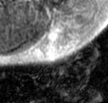
MRI of an extremity soft-tissue mass, one axial slice. Slice 33 of 42 in the series (ordered by position). T2-weighted fat-saturated. MR volume resampled by the dataset authors to the PET/CT grid (not the native acquisition matrix). 108 × 103 image matrix, field of view 105 × 101 mm. Male patient. From the clinical record (not read from this slice): histological type: leiomyosarcoma; grade: intermediate; site of the primary tumour: left pelvis.
Structures marked on this image (expert contour drawn on MRI and transferred to this co-registered scan by the dataset authors):
- gross tumour volume (mass): bounding box <37,24,68,56> (left, top, right, bottom; pixels)